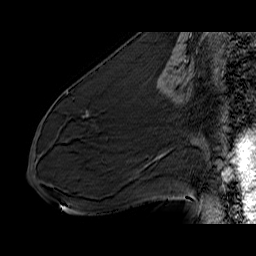
Breast MRI (dynamic contrast-enhanced), one sagittal slice. Slice 31 of 60 in the series (ordered by position). Dynamic contrast-enhanced series, time point 2 of 6 at this slice position (early post-contrast). 1.5 T. TE 6.5 ms, TR 32.9 ms. 4 mm slice thickness. 256 × 256 image matrix, field of view 200 × 200 mm. Female patient. Case-level facts recorded for this patient, not image findings: setting: breast cancer imaged before/during neoadjuvant chemotherapy; receptor status: HER2-positive.
Outlined on this slice (semi-automatic segmentation, software-assisted and operator-edited):
- analysis volume of interest (the breast-tissue region the enhancement analysis was run in; not a lesion): bounding box <72,88,133,137> (left, top, right, bottom; pixels)
- tumour enhancement mask (voxels above the 100 % enhancement threshold inside the analysis volume of interest): <86,112,89,117>